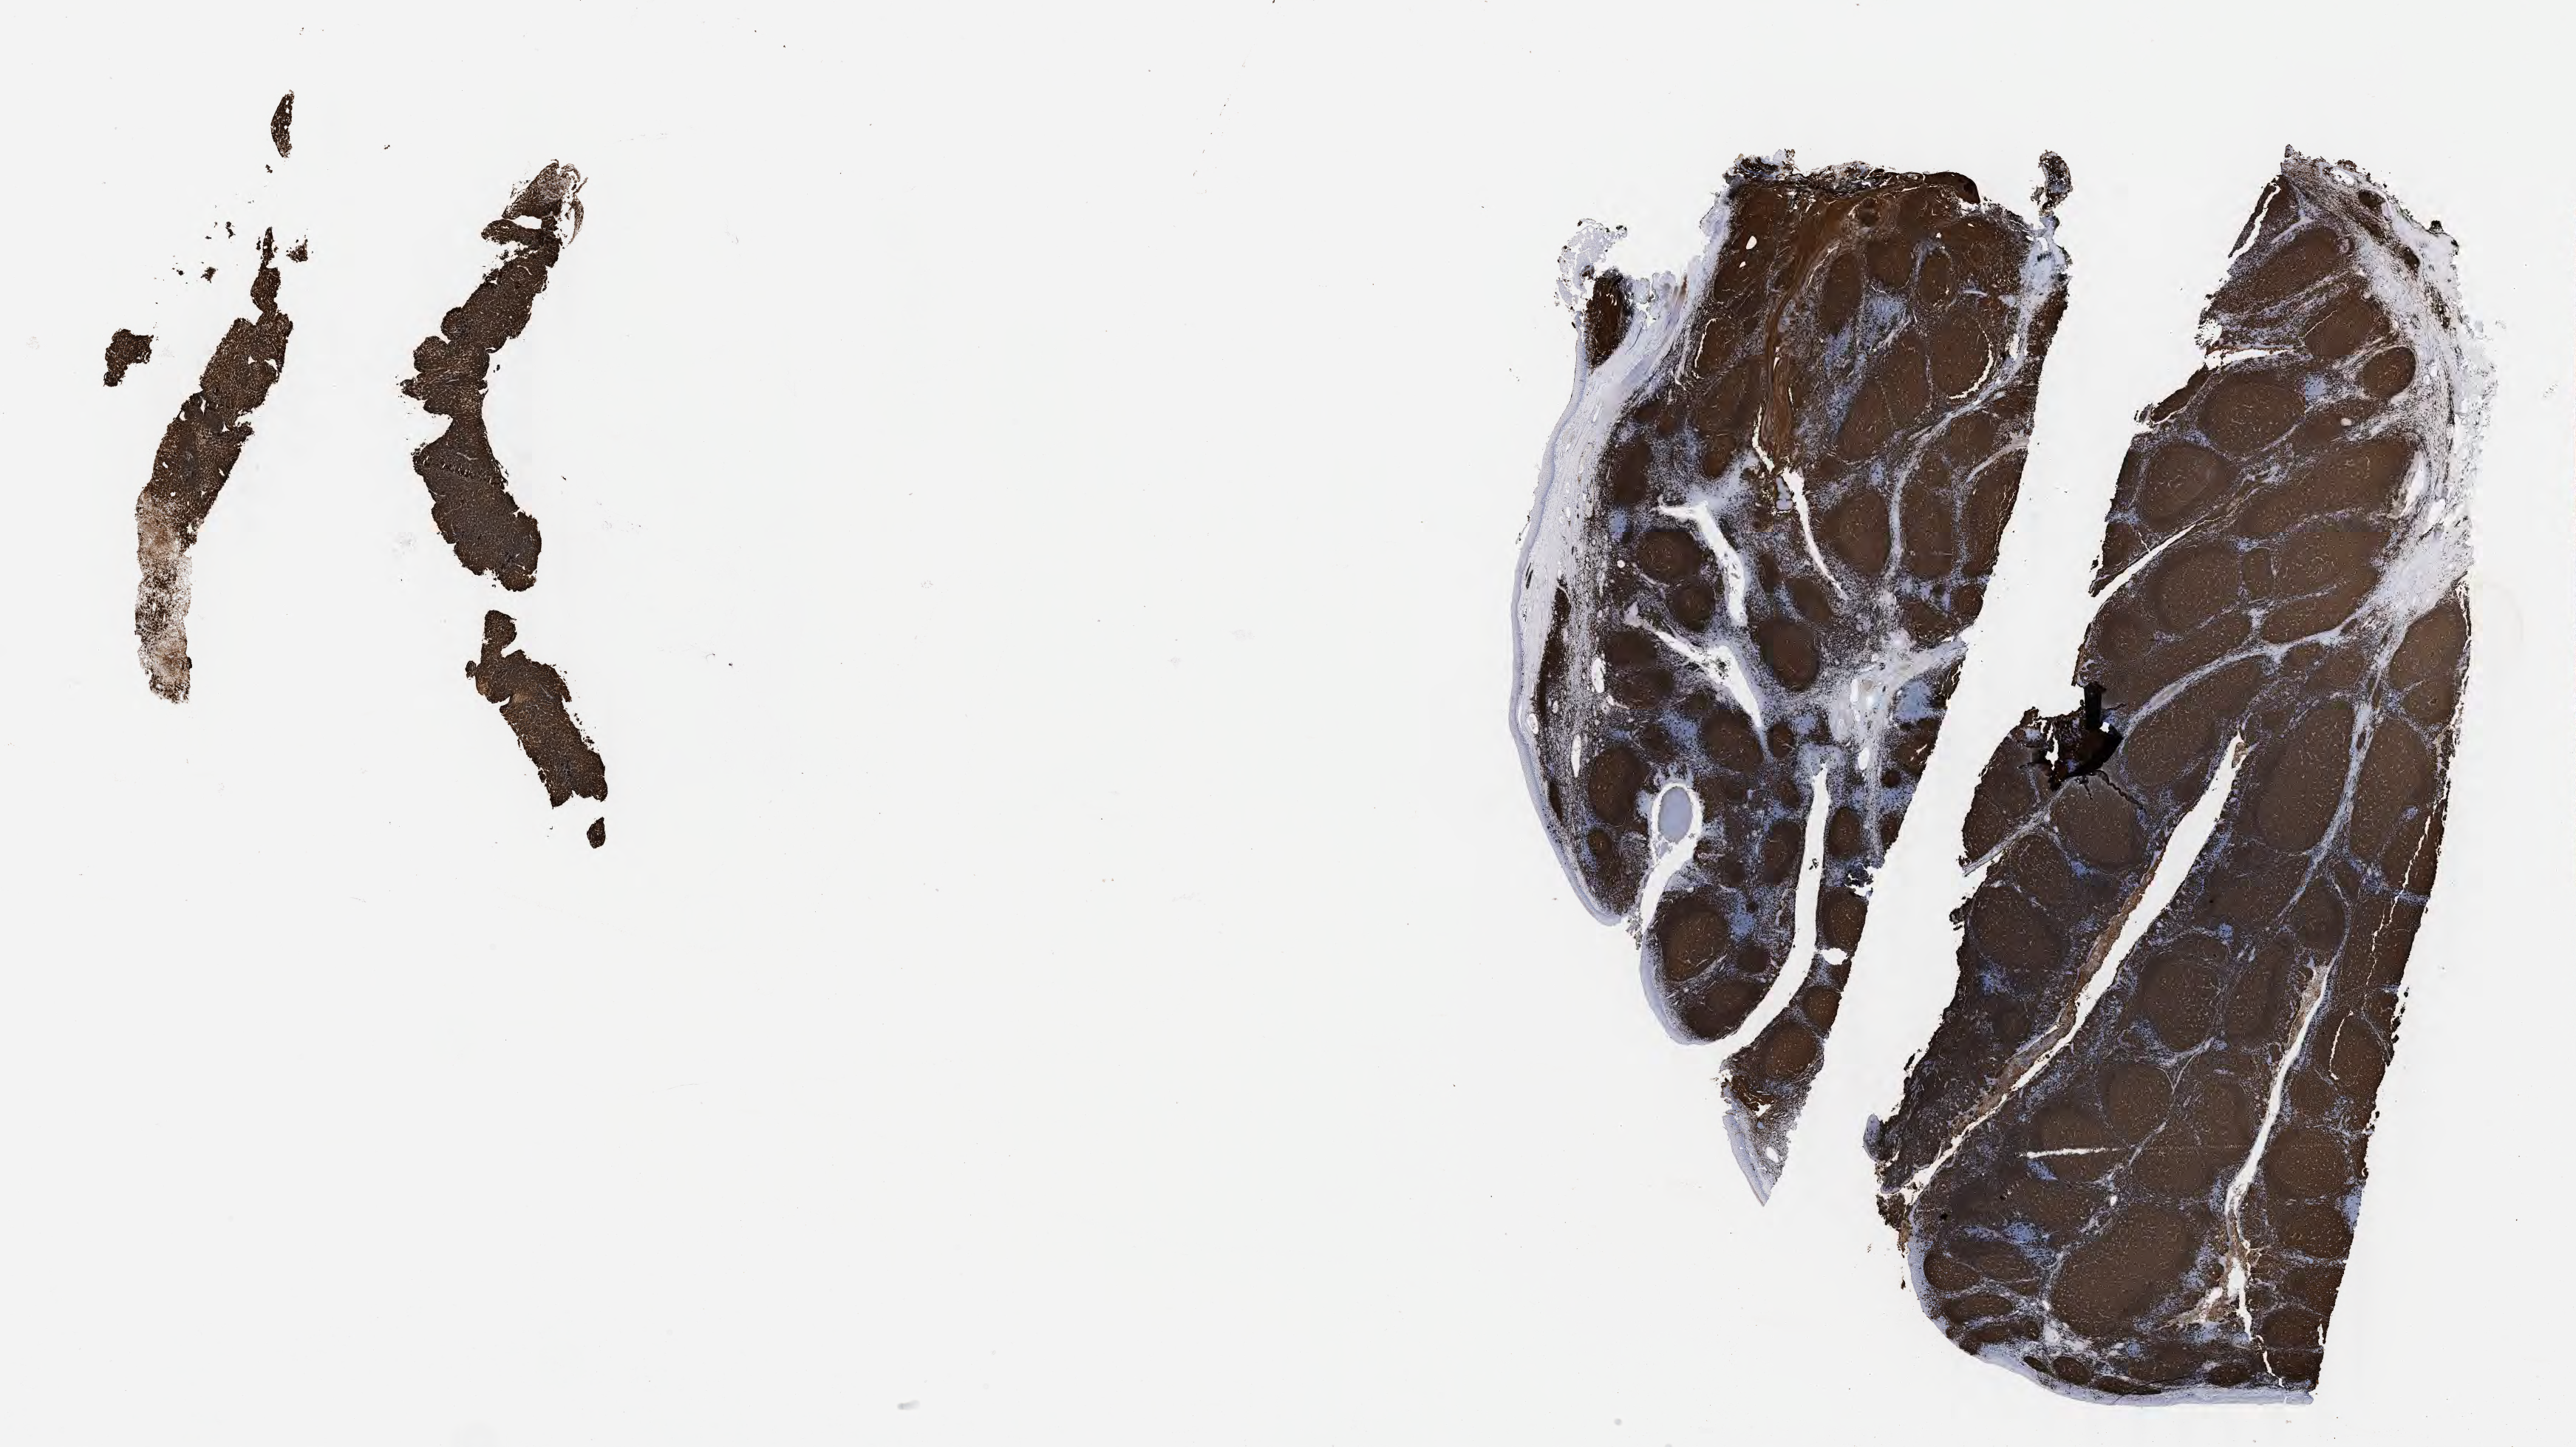
Whole-slide image, immunohistochemical stain for CD20, whole scanned area (about 28.2 x 15.8 mm) shown as a low-resolution overview, tumor tissue. Patient: female, aged 12.
Histologic diagnosis: Burkitt lymphoma, NOS.